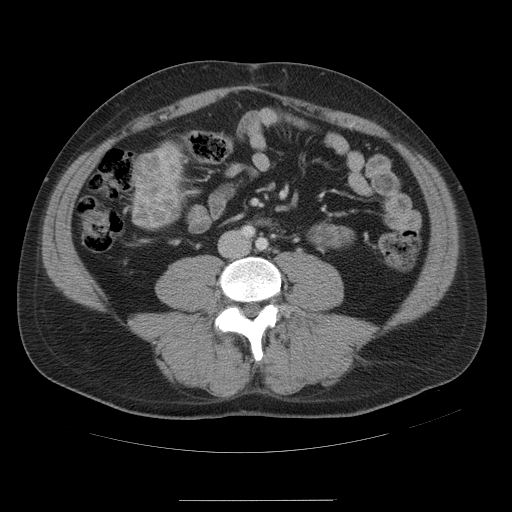
Contrast-enhanced abdominal CT, one axial slice; slice 5 of 54 in the series (ordered by position); 120 kVp; intravenous contrast given; soft-tissue window (W 400 / L 40 HU); 5 mm slice thickness; 512 × 512 image matrix. Male patient, age 40 years. From the clinical record (not read from this slice): diagnosis: colorectal cancer liver metastases, imaged before liver resection; multiple liver metastases: no; largest metastasis: 15 cm; chemotherapy before resection: no.
Annotated regions visible in this slice (manually delineated by an expert):
- liver: box from (x=131, y=145) to (x=184, y=228) px
- liver metastasis: (x=134, y=147)–(x=180, y=225)